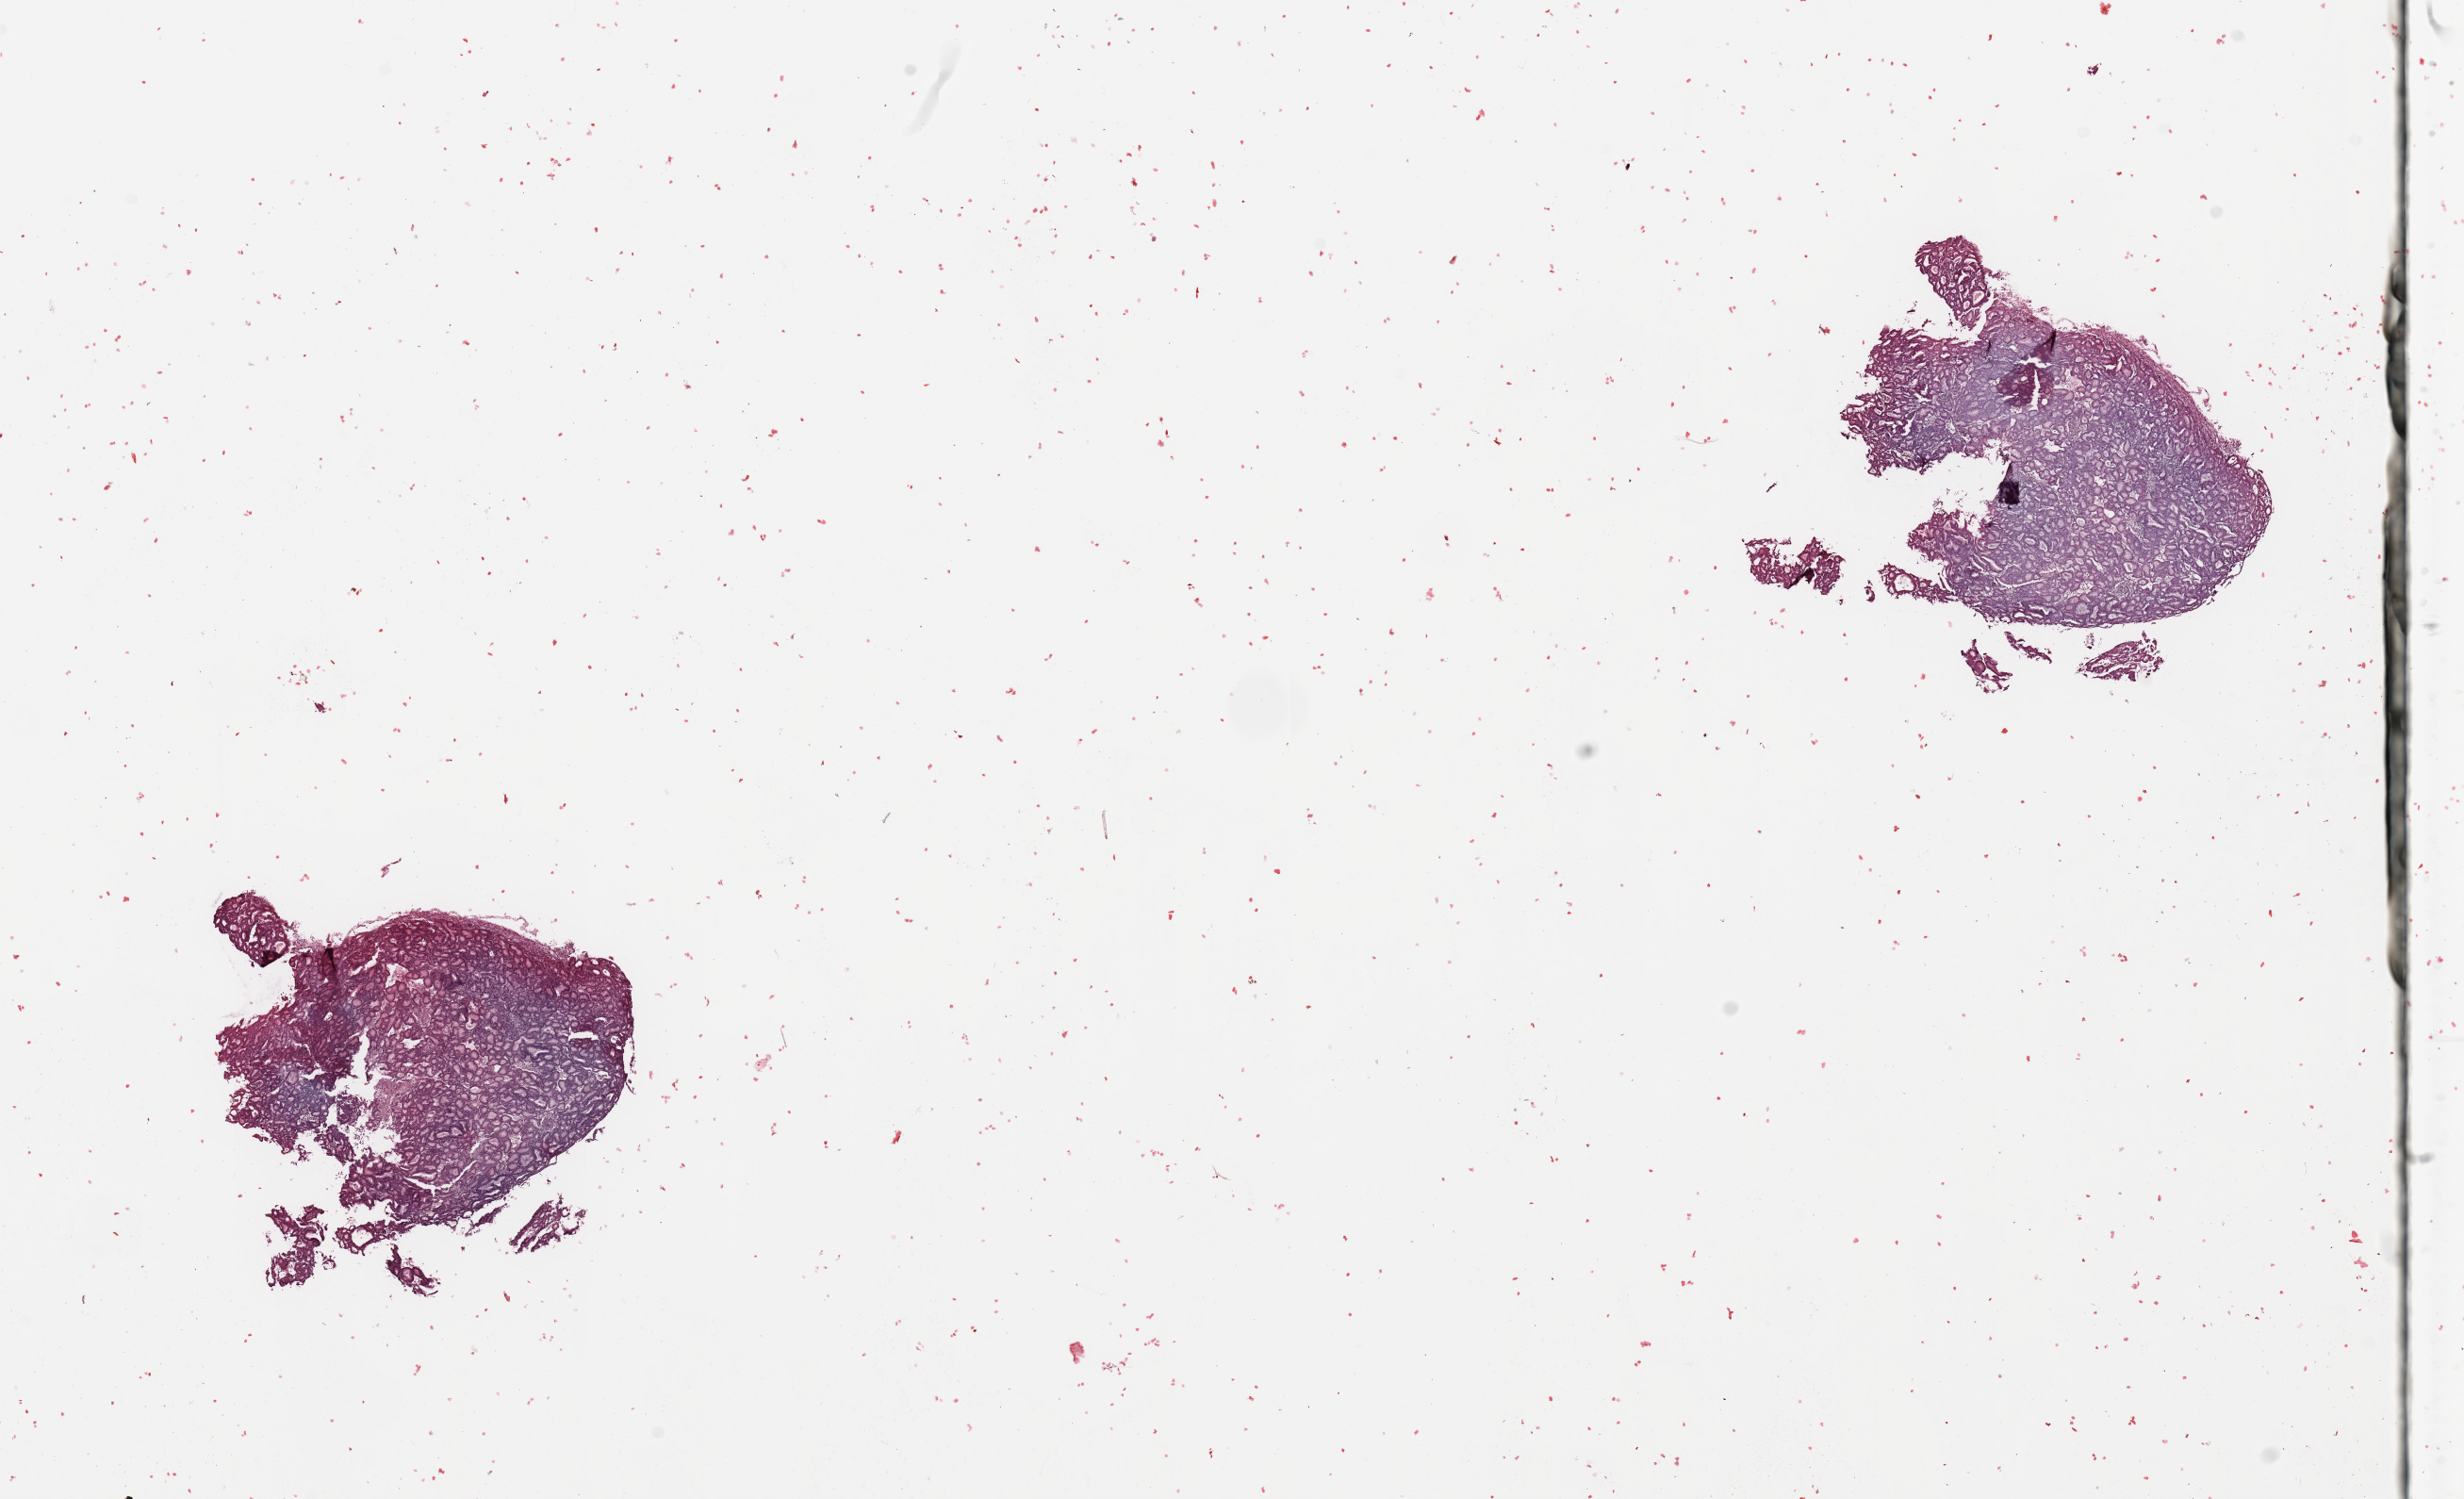
Digitized H&E tissue section (whole slide) — shown as a low-resolution overview of the whole scanned area (about 20.7 x 12.6 mm, from a 20x scan); tumour tissue sample, sampled site: uterus. Female, 71 y/o. Pathologist review of this section (percent, as recorded): tumour nuclei 90%, necrosis 2%.
Diagnosis: Endometrioid adenocarcinoma, NOS.